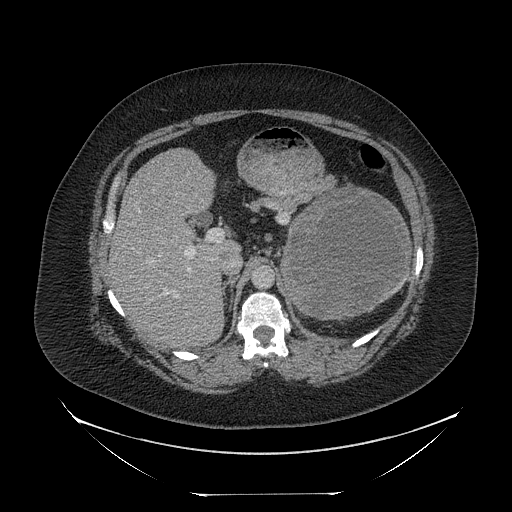
Contrast-enhanced abdominal CT, one axial slice; position 151 of 205 along the scan axis; reconstruction kernel STANDARD; soft-tissue window (W 400 / L 40 HU); 2.5 mm slice thickness; 512 × 512 image matrix. Female patient, age 53 years. Case-level facts recorded for this patient, not image findings: diagnosis: adrenocortical carcinoma; tumour side: left adrenal; tumour size at pathology: 17 cm; Ki-67 index: 20 %; stage (as recorded): 3.
Outlined on this slice (semi-automatically segmented with operator editing):
- mass: bounding box (x1, y1, x2, y2) in pixels: (285, 189, 410, 318)